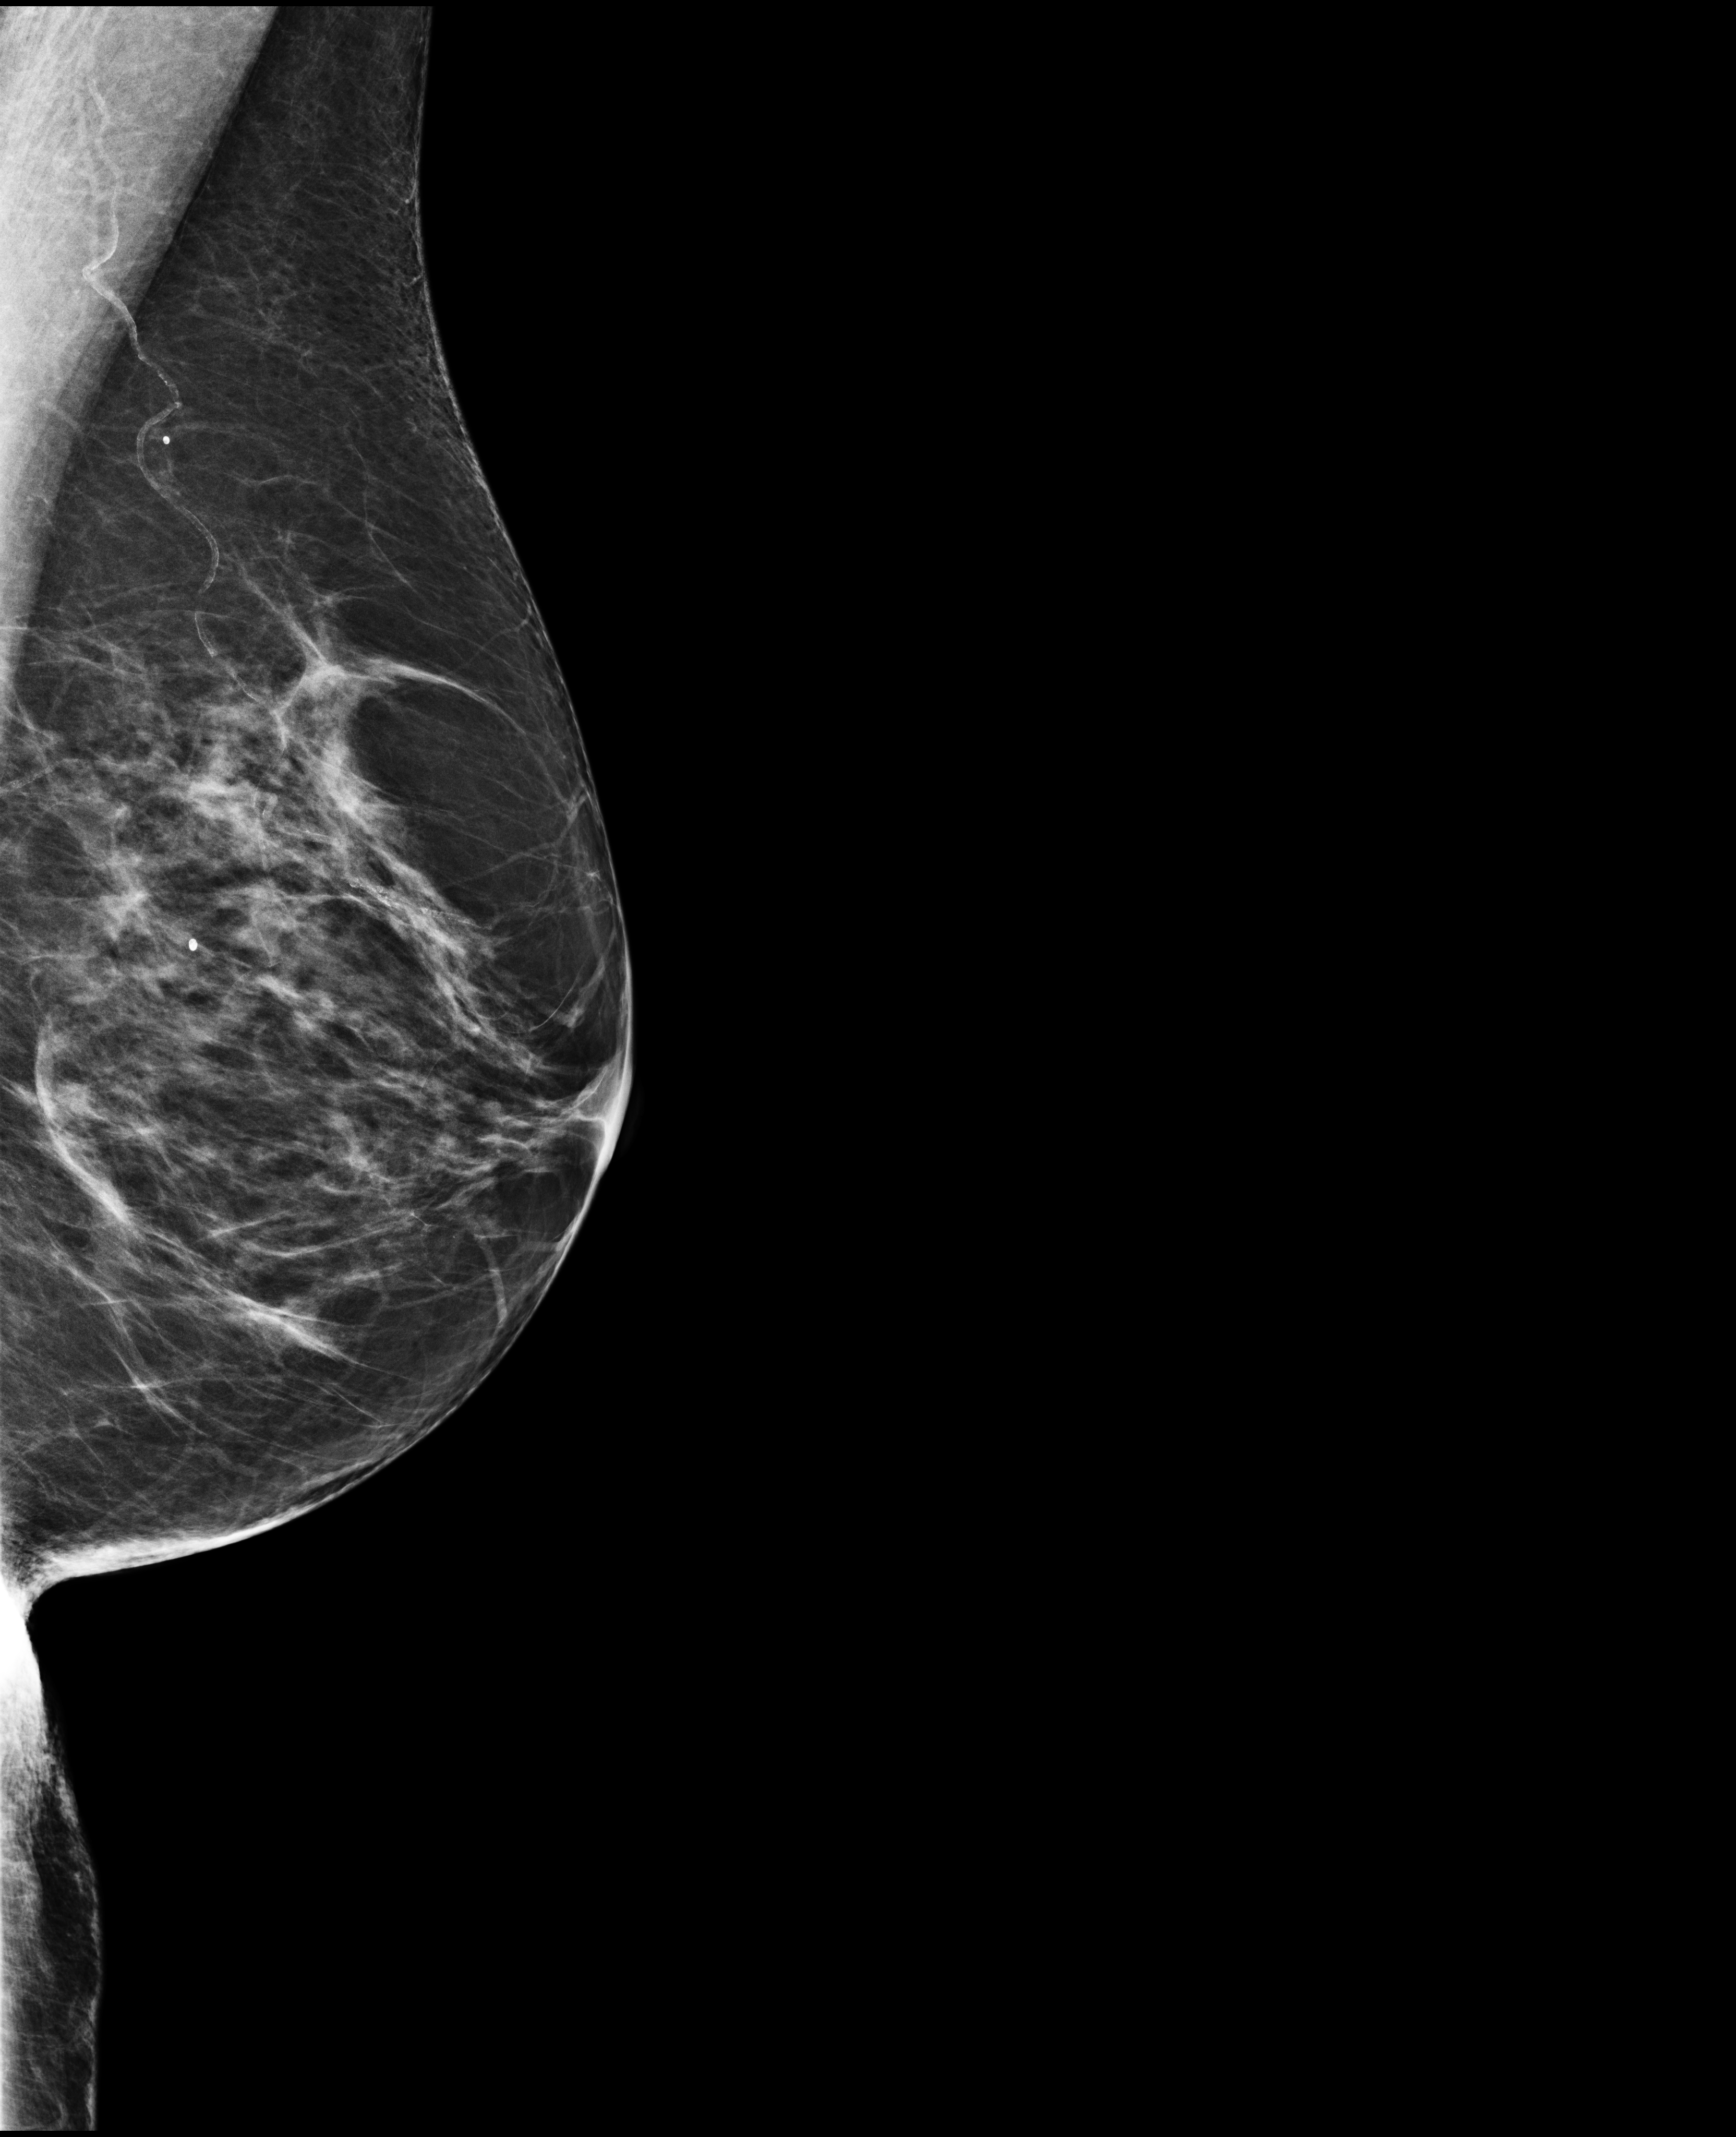
Full-field digital mammogram (FFDM), left breast, medio-lateral oblique projection, screening examination. Patient: female, 67 years.
Breast density at the screening exam (both breasts): heterogeneously dense (BI-RADS density category c). Final BI-RADS assessment for this screening round (tomosynthesis exam, both breasts): category 1. Recall: no recall after this screen.